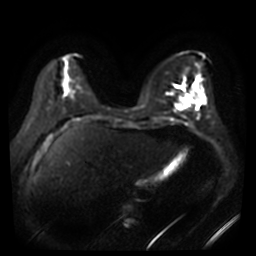
Breast MRI, one axial slice. Slice 15 of 44 in the series (ordered by position). Diffusion-weighted series; image 2 of 4 stored at this slice position (different b-values; order by instance number). 3 T. 5 mm slice thickness. 256 × 256 image matrix, field of view 360 × 360 mm. Female patient.
Structures marked on this image (outlined manually by an expert reader):
- tumour on diffusion-weighted imaging: box from (x=179, y=97) to (x=184, y=103) px